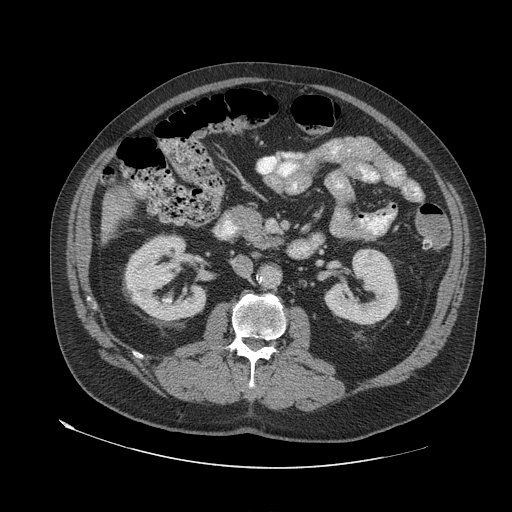
Contrast-enhanced abdominal CT (liver protocol), one axial slice. Slice 14 of 79 in the series (ordered by position). 140 kVp. Soft-tissue window (W 400 / L 40 HU). 512 × 512 image matrix, field of view 480 × 480 mm. From the clinical record (not read from this slice): diagnosis: hepatocellular carcinoma (patient treated with transarterial chemoembolisation; whether this scan precedes or follows treatment is not stated here); TNM stage (as recorded): Stage-IVA; Child-Pugh class: A; tumour differentiation: well differentiated; tumour nodularity: multinodular.
Annotated regions visible in this slice (semi-automatic segmentation, software-assisted and operator-edited):
- liver parenchyma outside the tumour (the mass and vessels are separate outlines, so this box may not span the whole liver): bounding box <100,206,117,242> (left, top, right, bottom; pixels)